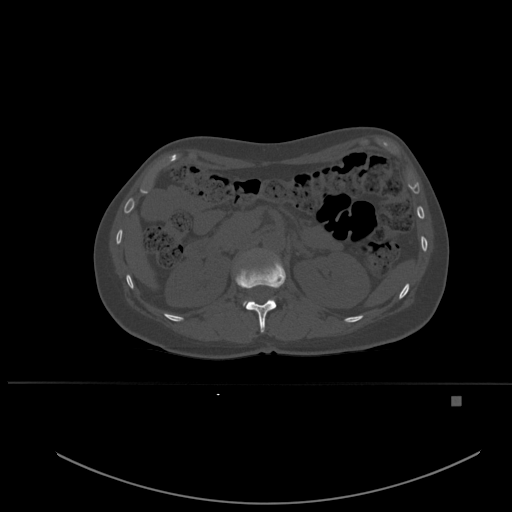
CT including the spine, one axial slice; position 248 of 651 along the scan axis; bone window (W 1800 / L 400 HU); 1.5 mm slice thickness; 512 × 512 image matrix. Patient: female, 49 years. Case-level facts recorded for this patient, not image findings: primary cancer: breast.
Annotated regions visible in this slice (semi-automatic segmentation, software-assisted and operator-edited):
- L1 vertebra: bounding box [x1, y1, x2, y2] px = [243, 301, 247, 305]
- T12 vertebra: [235, 257, 286, 333]